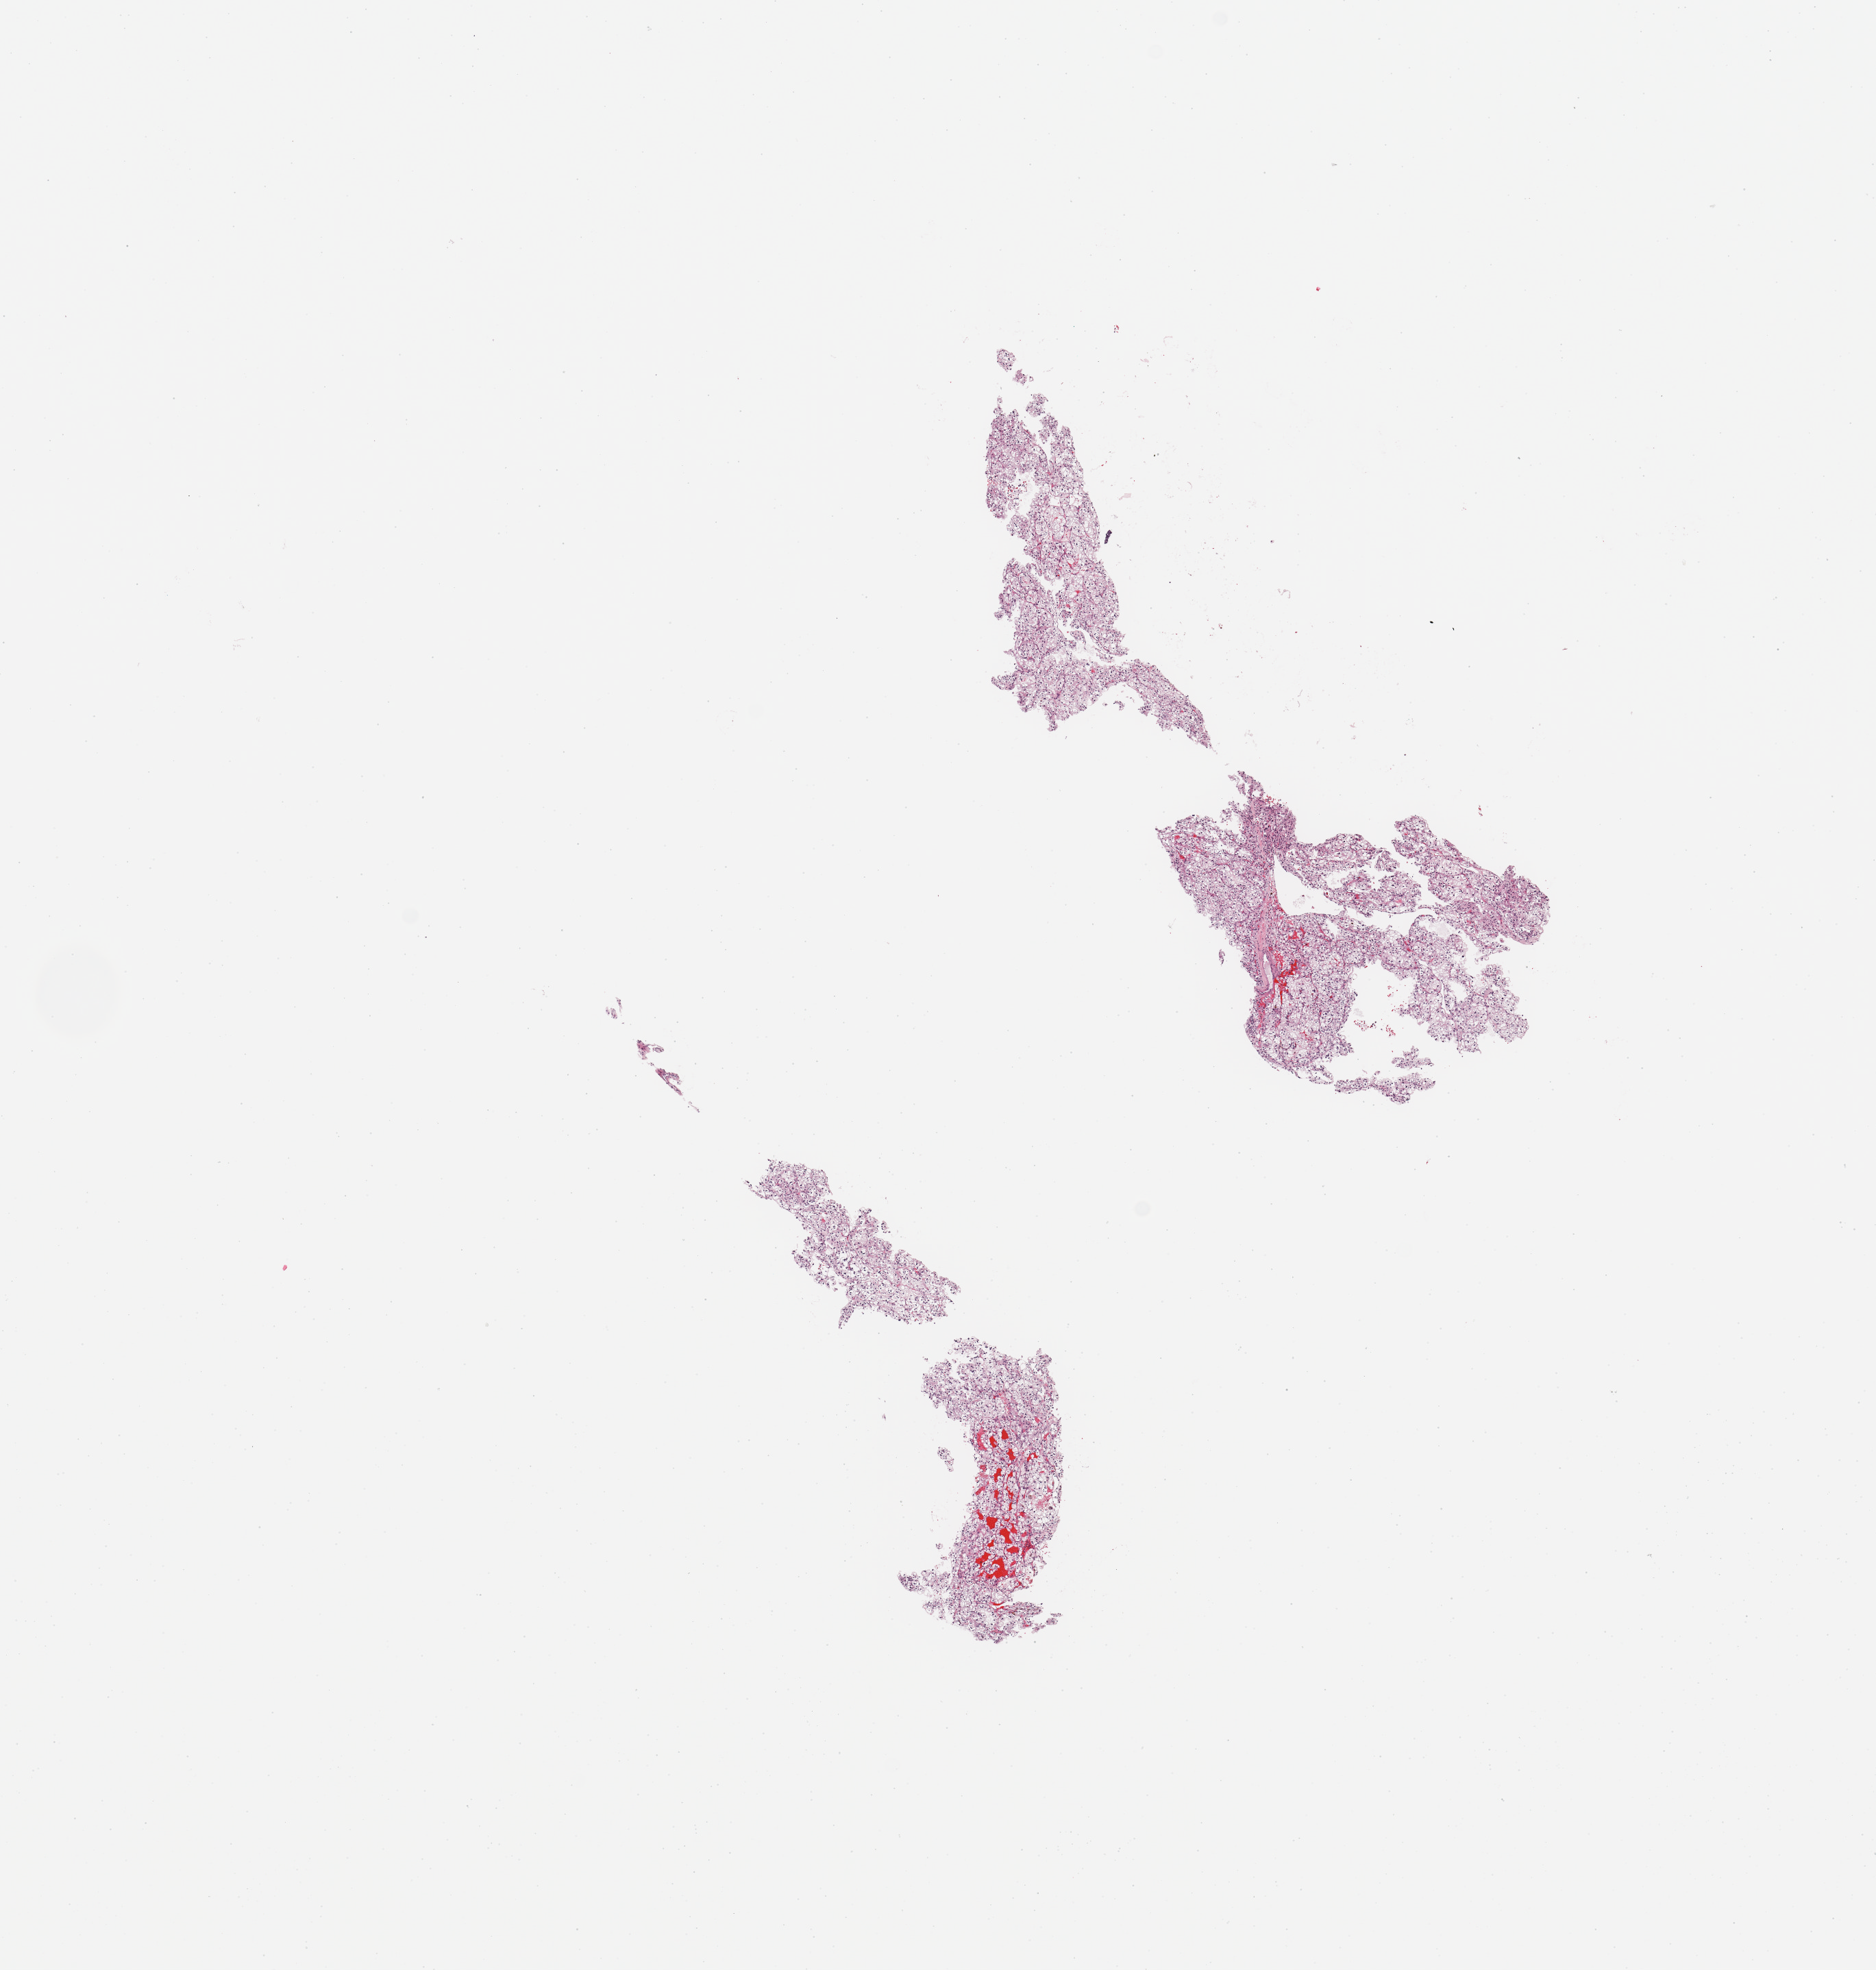
Hematoxylin and eosin (H&E) stained whole-slide image, a low-resolution overview of the entire scanned area, about 10.8 x 11.4 mm (slide scanned at 20x), tumour tissue sample, sampled site: kidney. Male, 85 y/o. Histologic grade: G2 (moderately differentiated). Pathologist review of this section (percent, as recorded): tumour nuclei 85%, necrosis 0%.
• primary tumour site (as recorded): lower pole
• diagnosis: Renal cell carcinoma, NOS
• AJCC pathologic stage: III